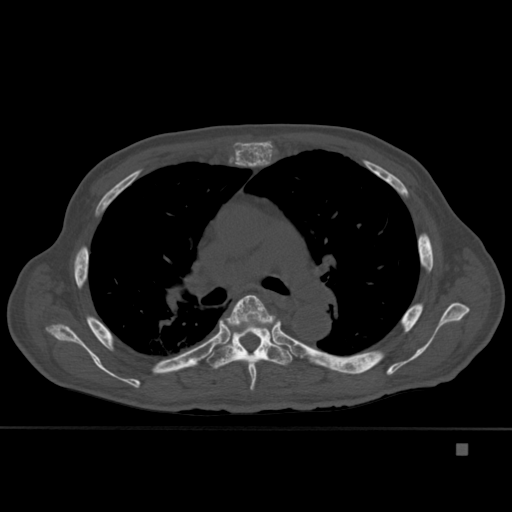
CT including the spine, one axial slice. Slice 299 of 451 in the series (ordered by position). Bone window (W 1800 / L 400 HU). 512 × 512 image matrix. Male patient, age 75 years. From the clinical record (not read from this slice): primary cancer: prostate.
Annotated regions visible in this slice (semi-automatically segmented with operator editing):
- T5 vertebra: bounding box [x1, y1, x2, y2] px = [219, 295, 281, 391]
- T6 vertebra: [207, 317, 293, 369]